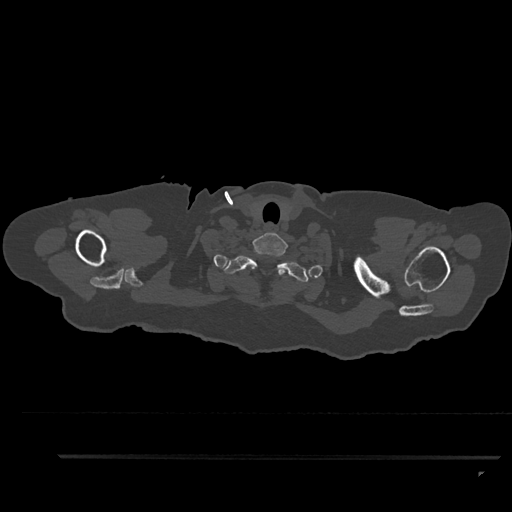
CT including the spine, one axial slice; position 776 of 797 along the scan axis; 120 kVp; bone window (W 1800 / L 400 HU); 0.5 mm slice thickness; 512 × 512 image matrix, field of view 408 × 408 mm. Female patient, age 44 years. From the clinical record (not read from this slice): primary cancer: renal; vertebrae with lytic lesions (as recorded): L1.
Outlined on this slice (semi-automatically segmented with operator editing):
- T1 vertebra: box from (x=224, y=246) to (x=309, y=282) px